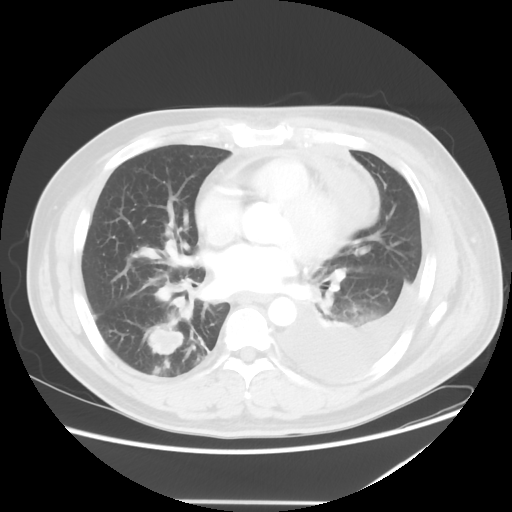
Chest CT, one axial slice; slice 23 of 52 in the series (ordered by position); lung window (W 1500 / L -600 HU); 5 mm slice thickness; 512 × 512 image matrix, field of view 405 × 405 mm. Male patient, age 42 years. Case-level facts recorded for this patient, not image findings: clinical TNM (as recorded): T2 N1 M1.
Outlined on this slice (bounding box drawn by a radiologist):
- lung tumour (recorded histology: adenocarcinoma): bounding box <145,324,188,364> (left, top, right, bottom; pixels)